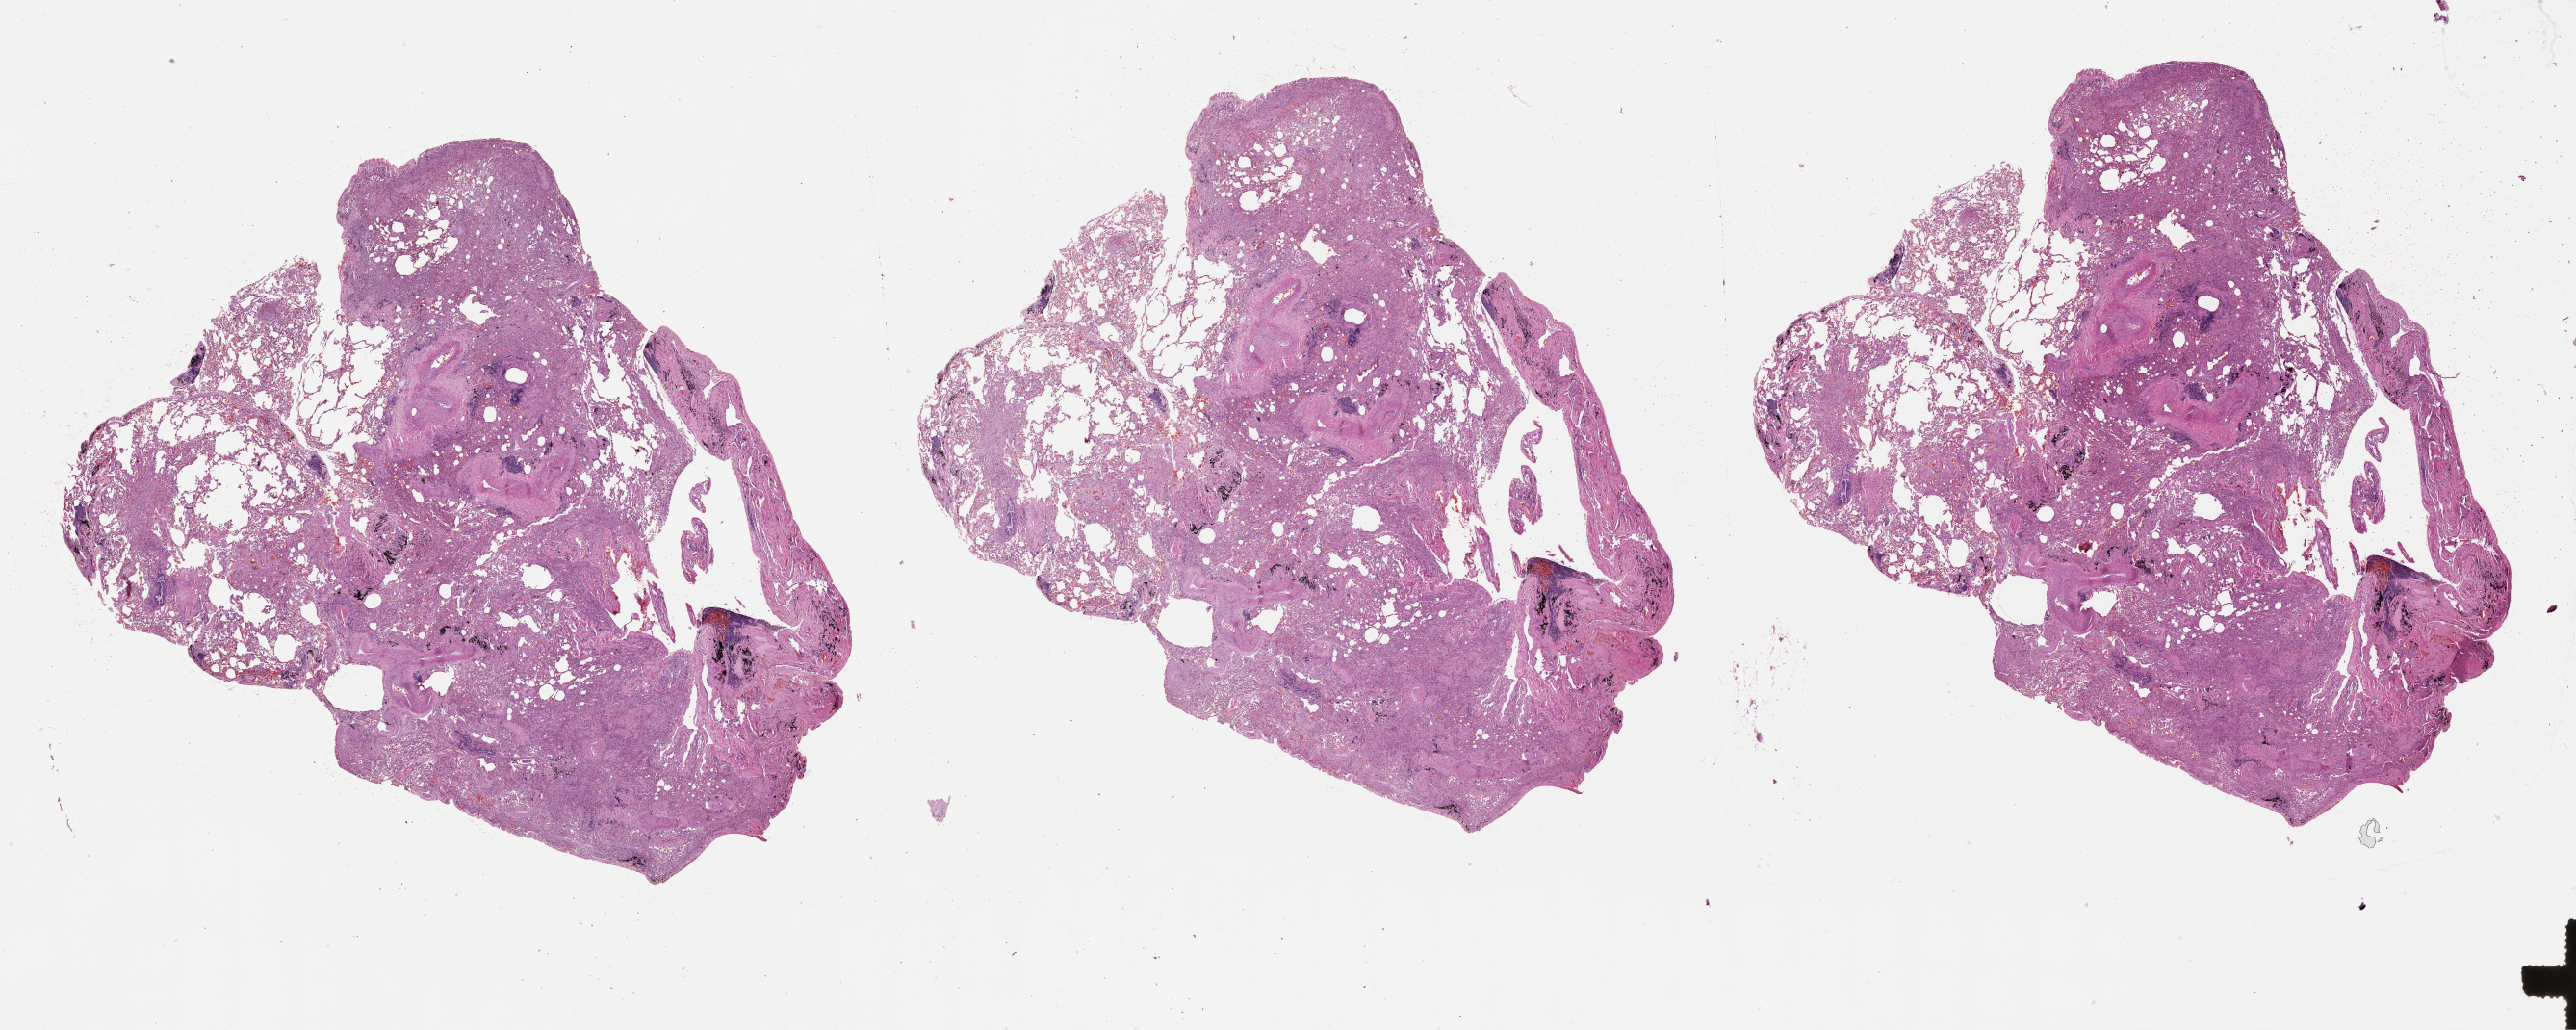
Digitized H&E-stained tissue section (whole slide) — shown as a low-resolution overview of the whole scanned area (about 43.1 x 17.2 mm), normal (non-tumour) tissue sample, lung. 74-year-old male patient.
* this section: normal (non-tumour) tissue from the same patient
* patient diagnosis (cohort enrolment): squamous cell carcinoma (lung)